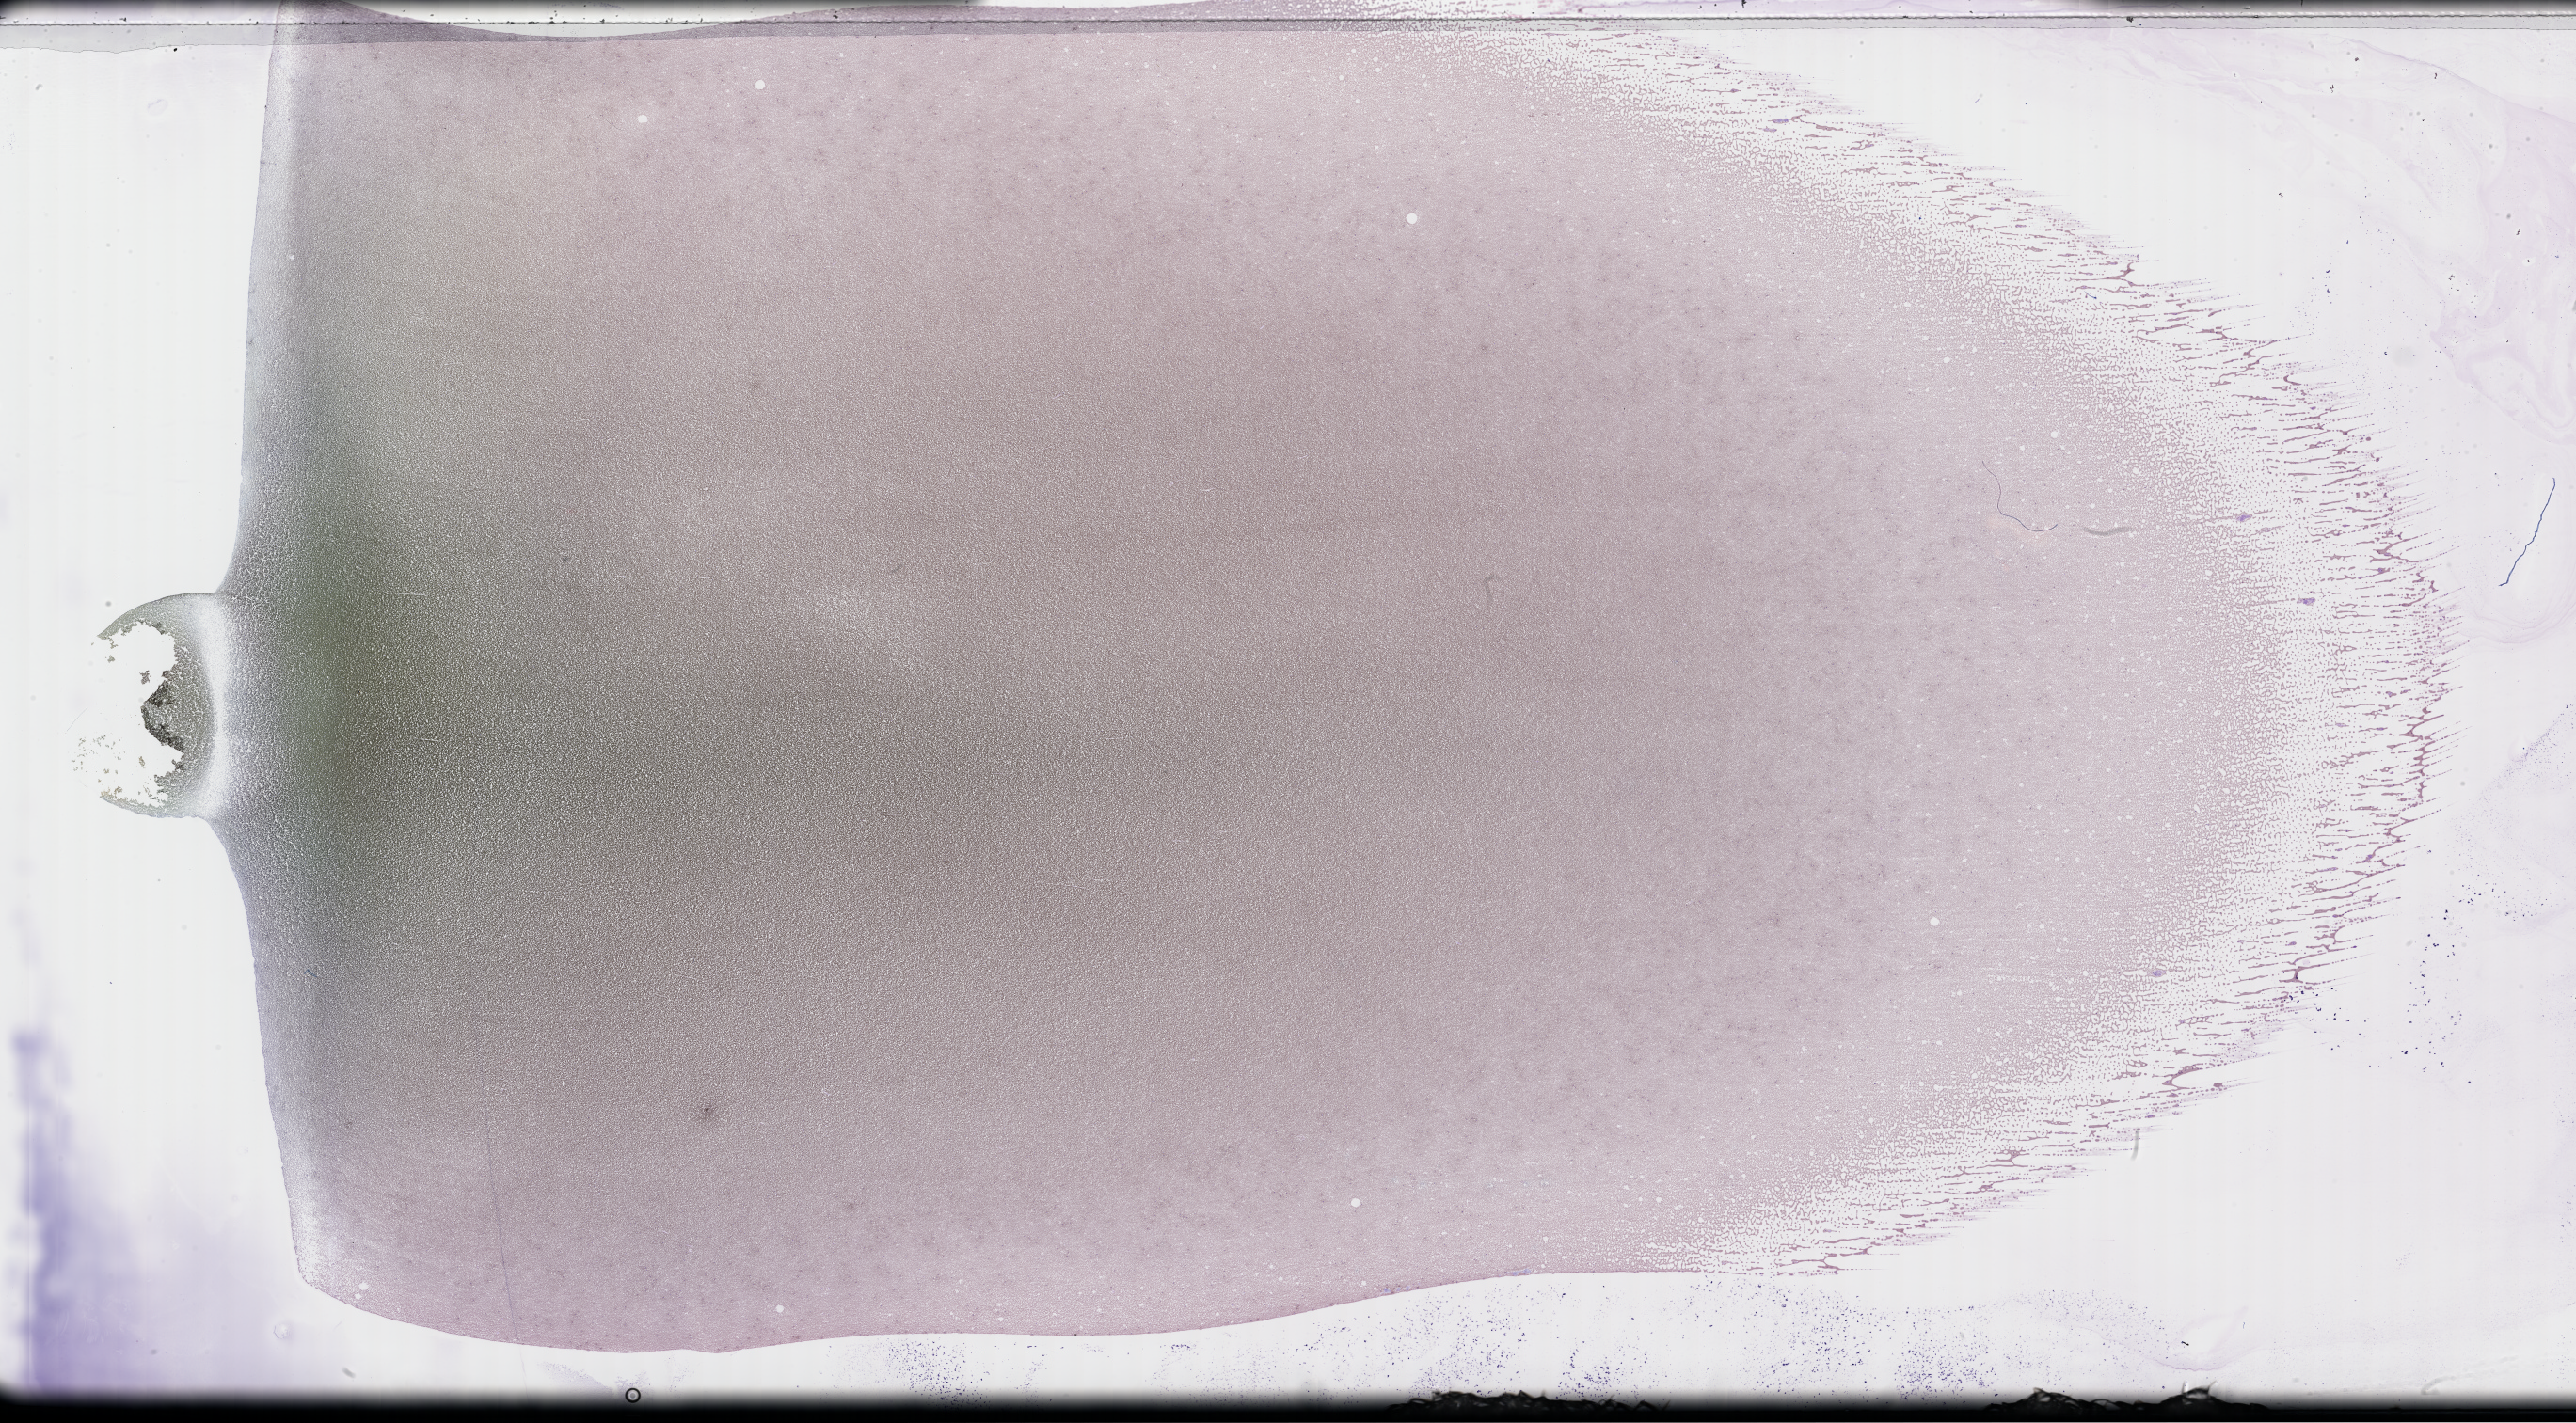
Wright-Giemsa-stained whole blood smear, whole-slide image — whole scanned area (about 44.2 x 24.4 mm) shown as a low-resolution overview; smear from an EDTA sample. Male patient.
Patient diagnosis: Plasma Cell Myeloma.